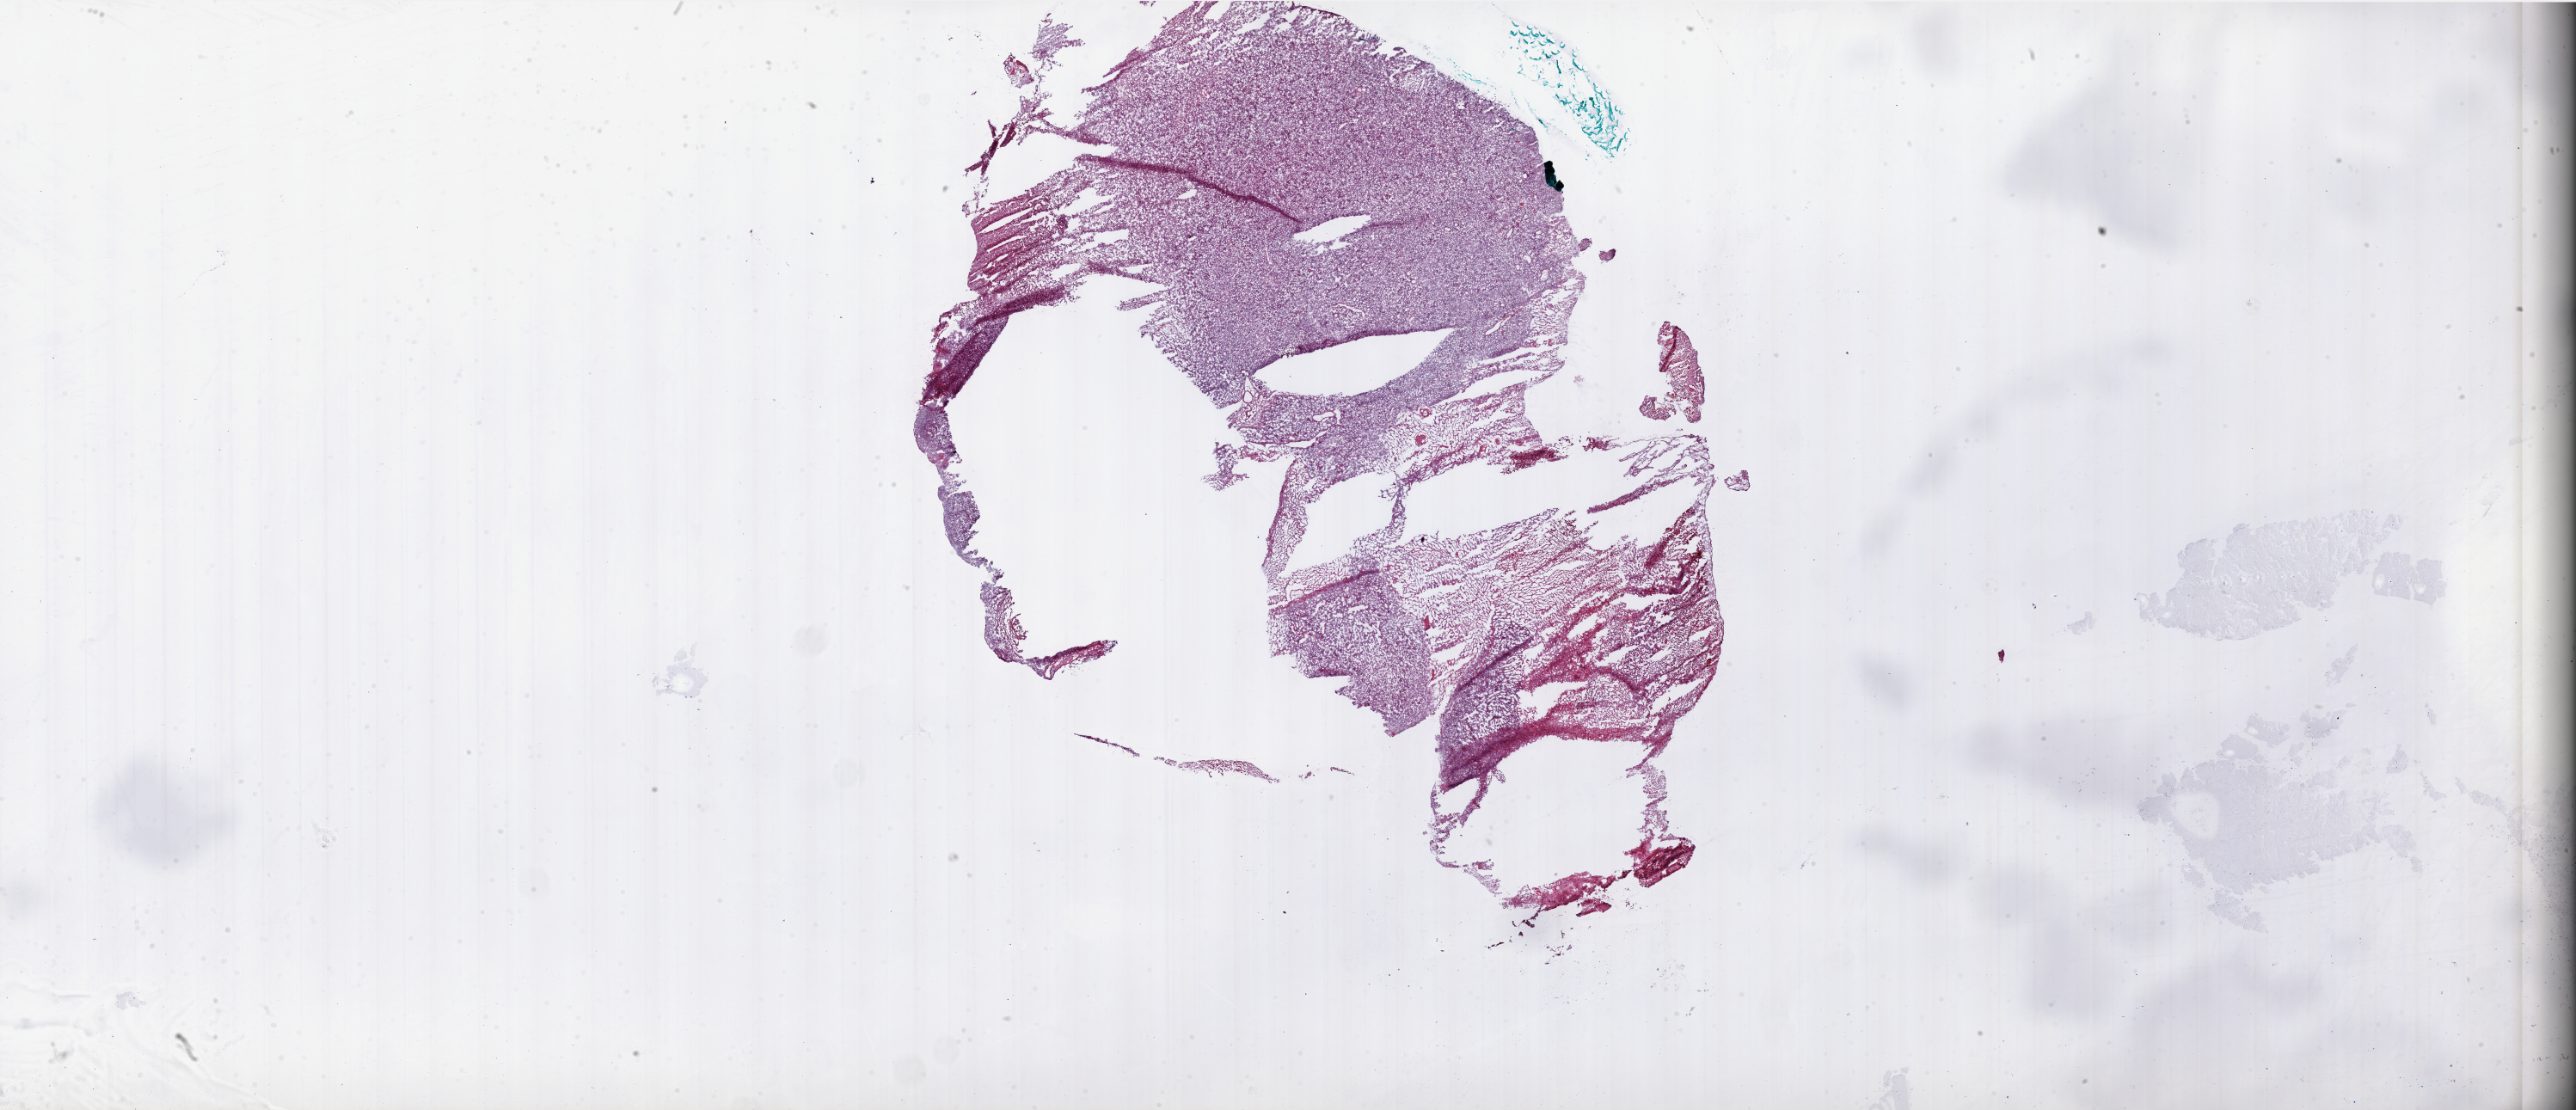
Whole-slide histology image, Hematoxylin and eosin (H&E) stained, whole scanned area (about 48.0 x 20.7 mm, acquisition: 20x scan) shown as a low-resolution overview; frozen section; primary tumour sample from the brain. Patient: female, age at initial diagnosis 77 years.
Histologic diagnosis: Glioblastoma.